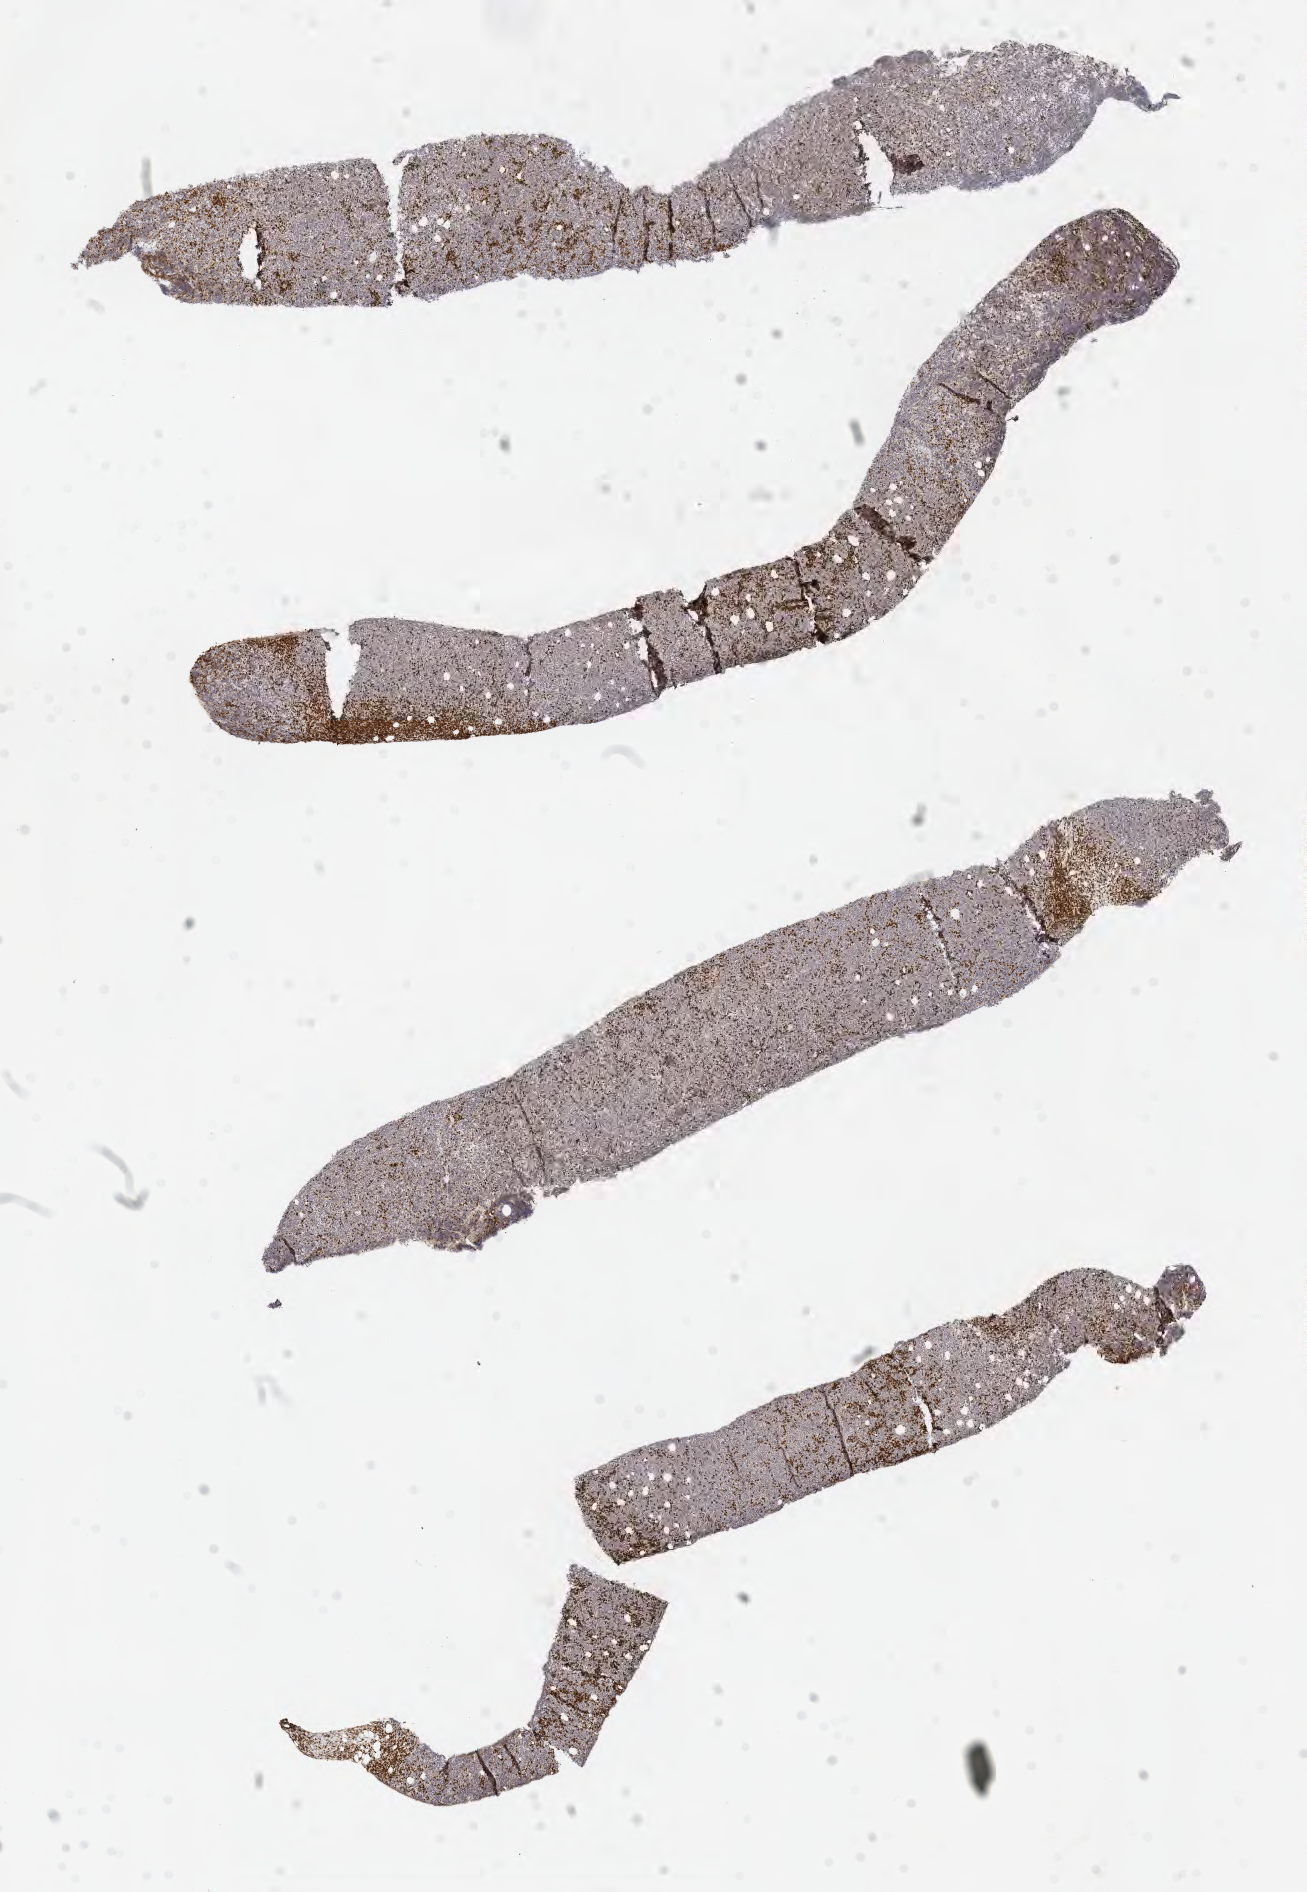
IHC for CD3, whole-slide image, shown as a low-resolution overview of the whole scanned area (about 10.6 x 15.3 mm). Tumor tissue. Male patient, age 69 years.
Histologic diagnosis: Diffuse large B-cell lymphoma, NOS.